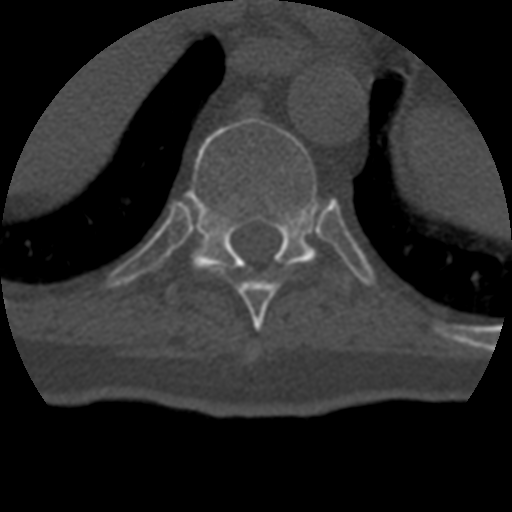
CT including the spine, one axial slice; slice 228 of 399 in the series (ordered by position); reconstruction kernel STANDARD; 120 kVp; bone window (W 1800 / L 400 HU); 1.25 mm slice thickness; 512 × 512 image matrix. Patient age 69 years. Case-level facts recorded for this patient, not image findings: primary cancer: prostate.
Annotated regions visible in this slice (semi-automatic segmentation, software-assisted and operator-edited):
- T10 vertebra: bounding box [x1, y1, x2, y2] px = [168, 118, 349, 303]
- T9 vertebra: [237, 264, 299, 324]